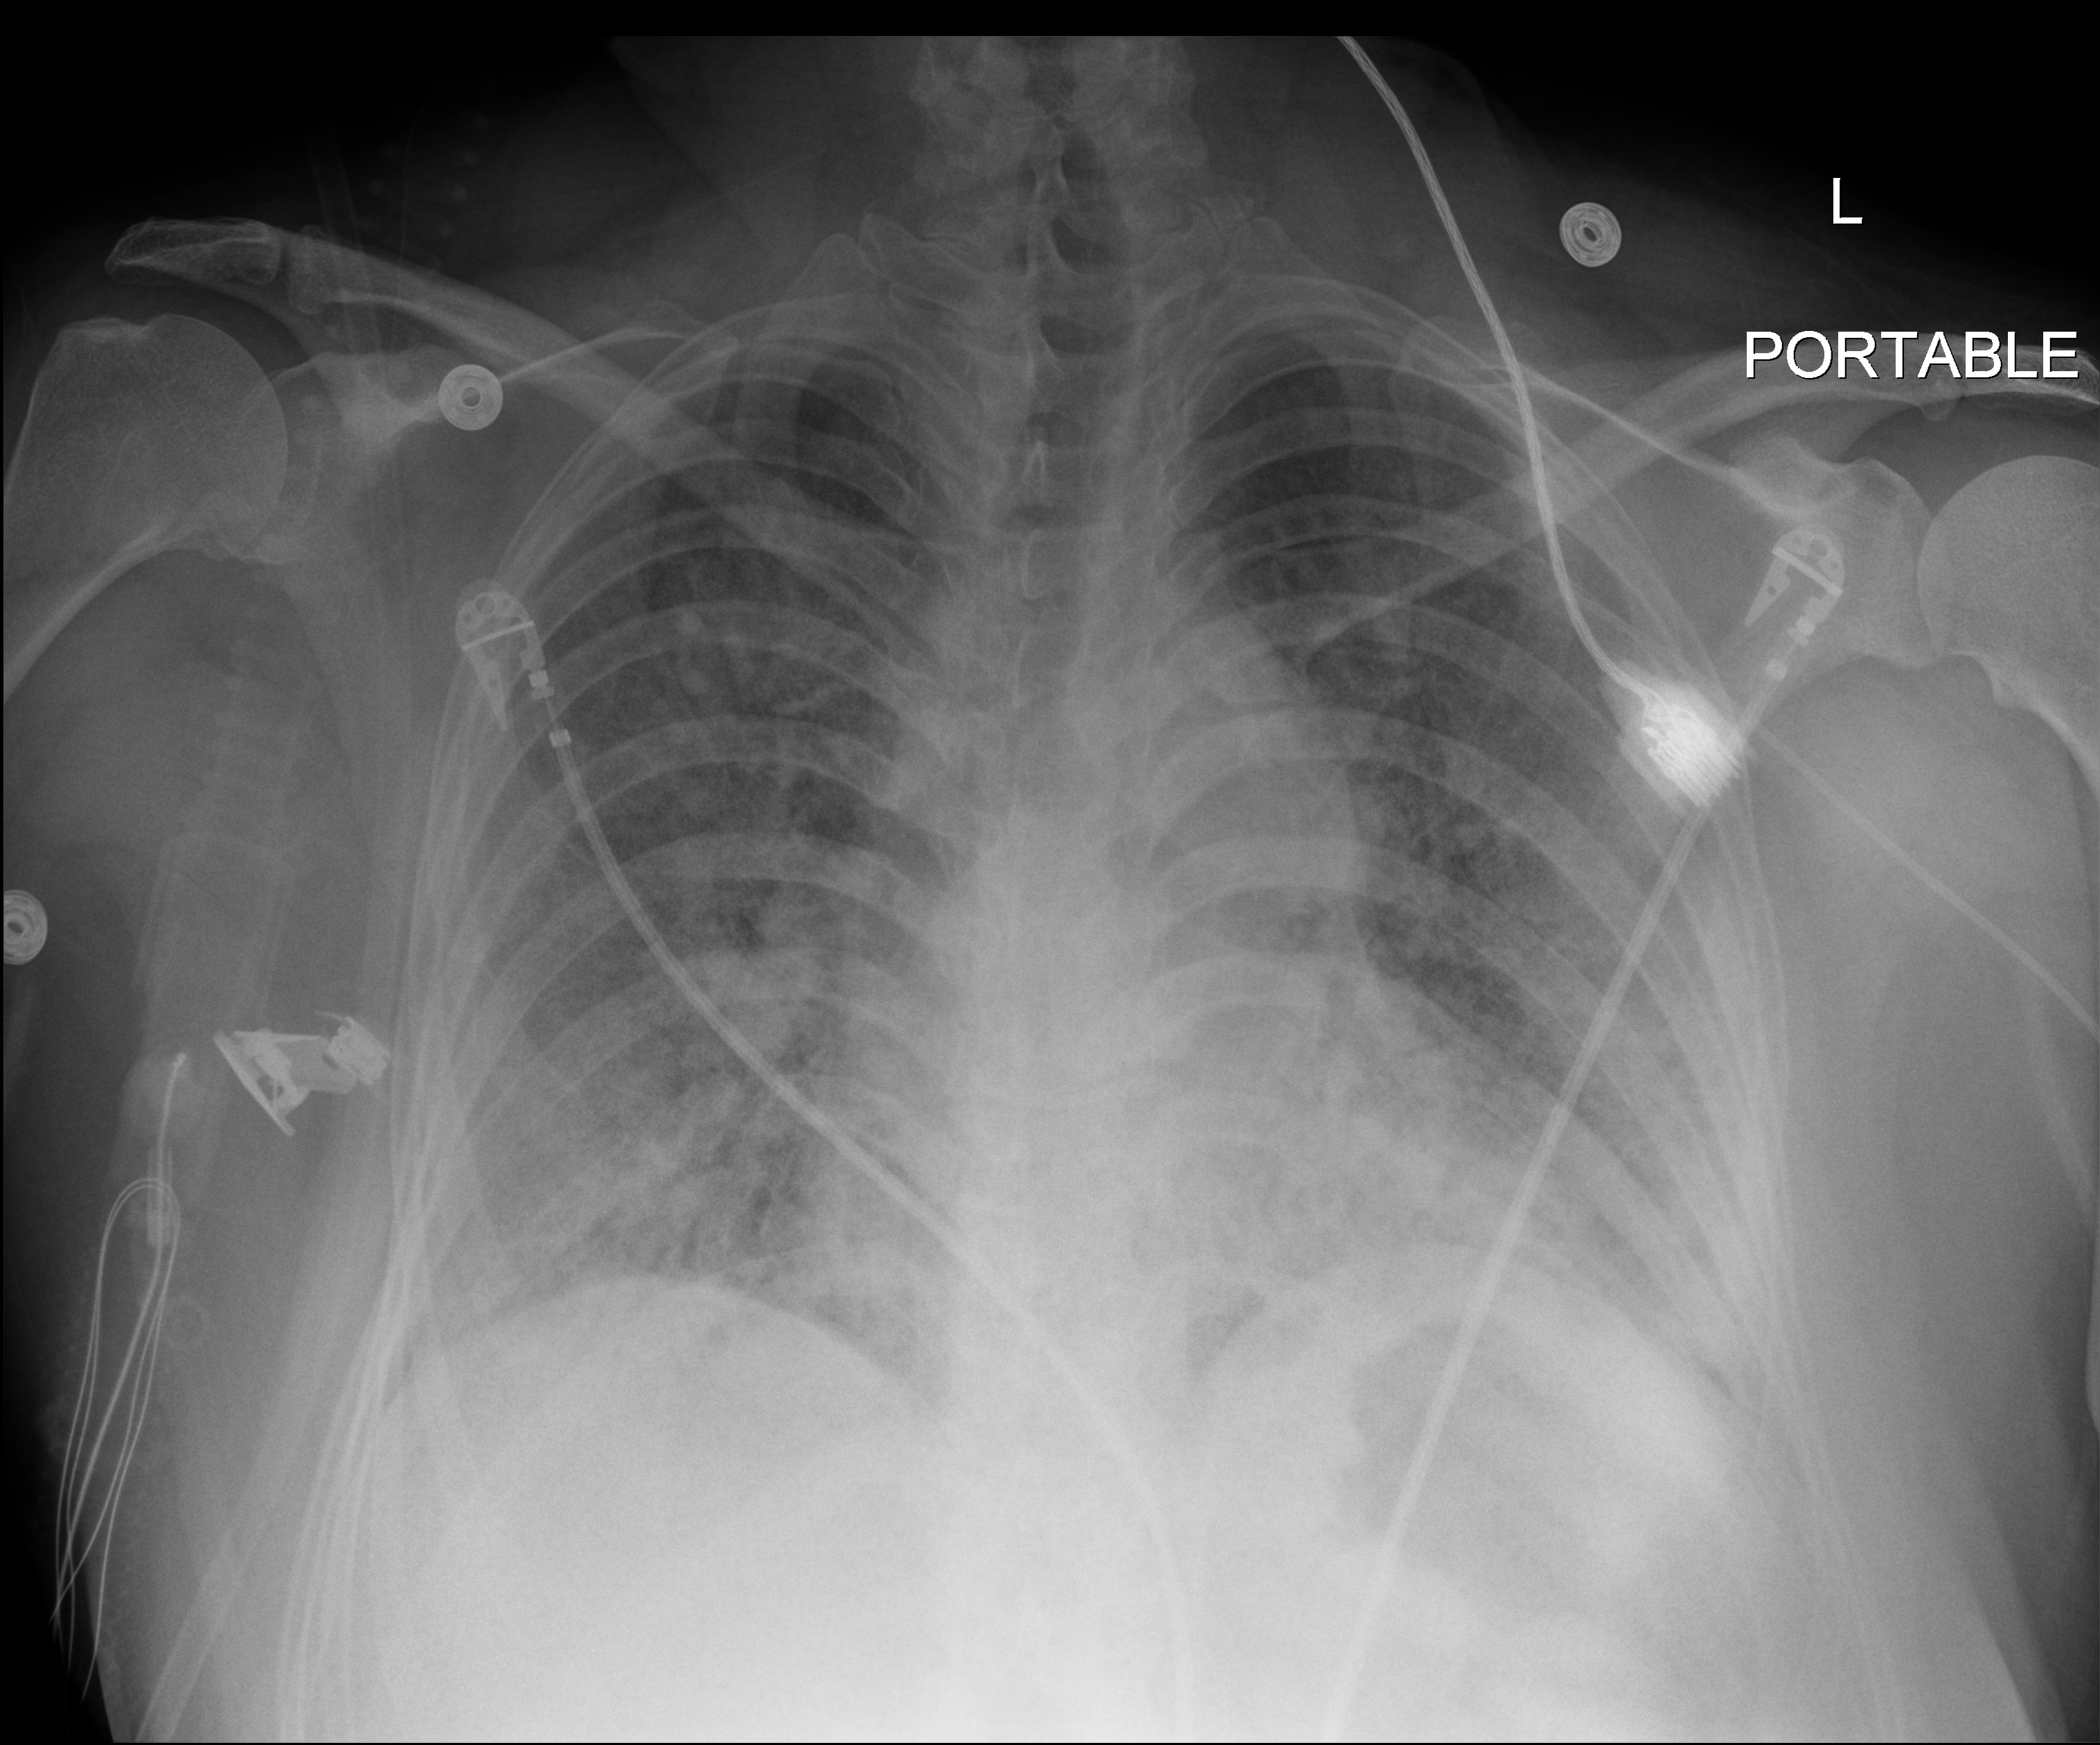
Chest X-ray (portable), anteroposterior (AP) projection. Adult patient hospitalised with COVID-19, age 18–59 years.
Admission-level facts for this patient (not findings on this image; timing relative to this image not recorded):
- mechanically ventilated during this hospital stay: yes